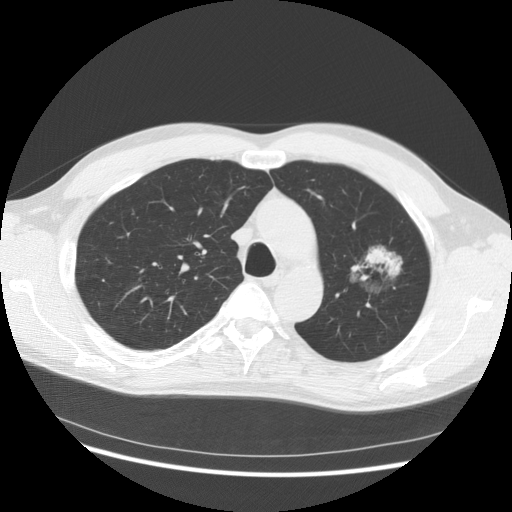
Low-dose screening chest CT, axial slice; third annual screen; lung window (W 1500 / L -600 HU); standard (soft-tissue) reconstruction kernel (STANDARD); 512 × 512 image matrix, field of view 370 × 370 mm. Male, age 61 years at enrolment.
Expert-annotated lung lesion, box from (x=332, y=229) to (x=411, y=309) px. Reader record for this screening exam (exam-level; its link to the box is not recorded): non-calcified nodule or mass ≥4 mm, left upper lobe, 37 × 33 mm, poorly defined margins, mixed attenuation, pre-existing on the prior screen: yes; interval growth: yes. Lung cancer was diagnosed 361 days after this screen: bronchiolo-alveolar adenocarcinoma, NOS, left upper lobe, well differentiated (G1), stage IB (AJCC 6th edition), 44 mm at pathology.